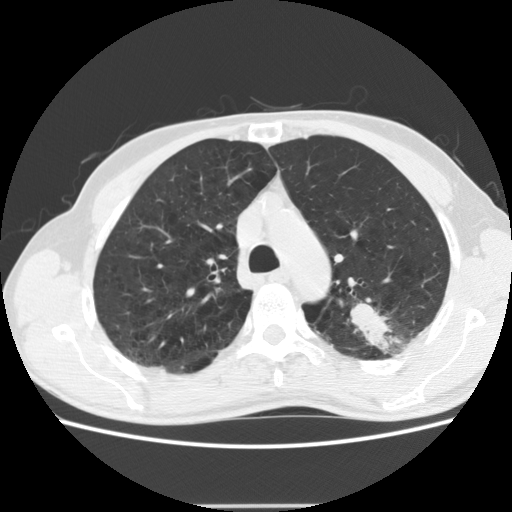
Low-dose screening chest CT, one axial slice. Slice 143 of 191 in the series (ordered by position). Reconstruction kernel STANDARD. 120 kVp. Lung window (W 1500 / L -600 HU). 2.5 mm slice thickness. 512 × 512 image matrix, field of view 352 × 352 mm.
Outlined on this slice (expert manual segmentation):
- lesion 1 (tumor, upper lobe of left lung): box from (x=351, y=303) to (x=390, y=347) px